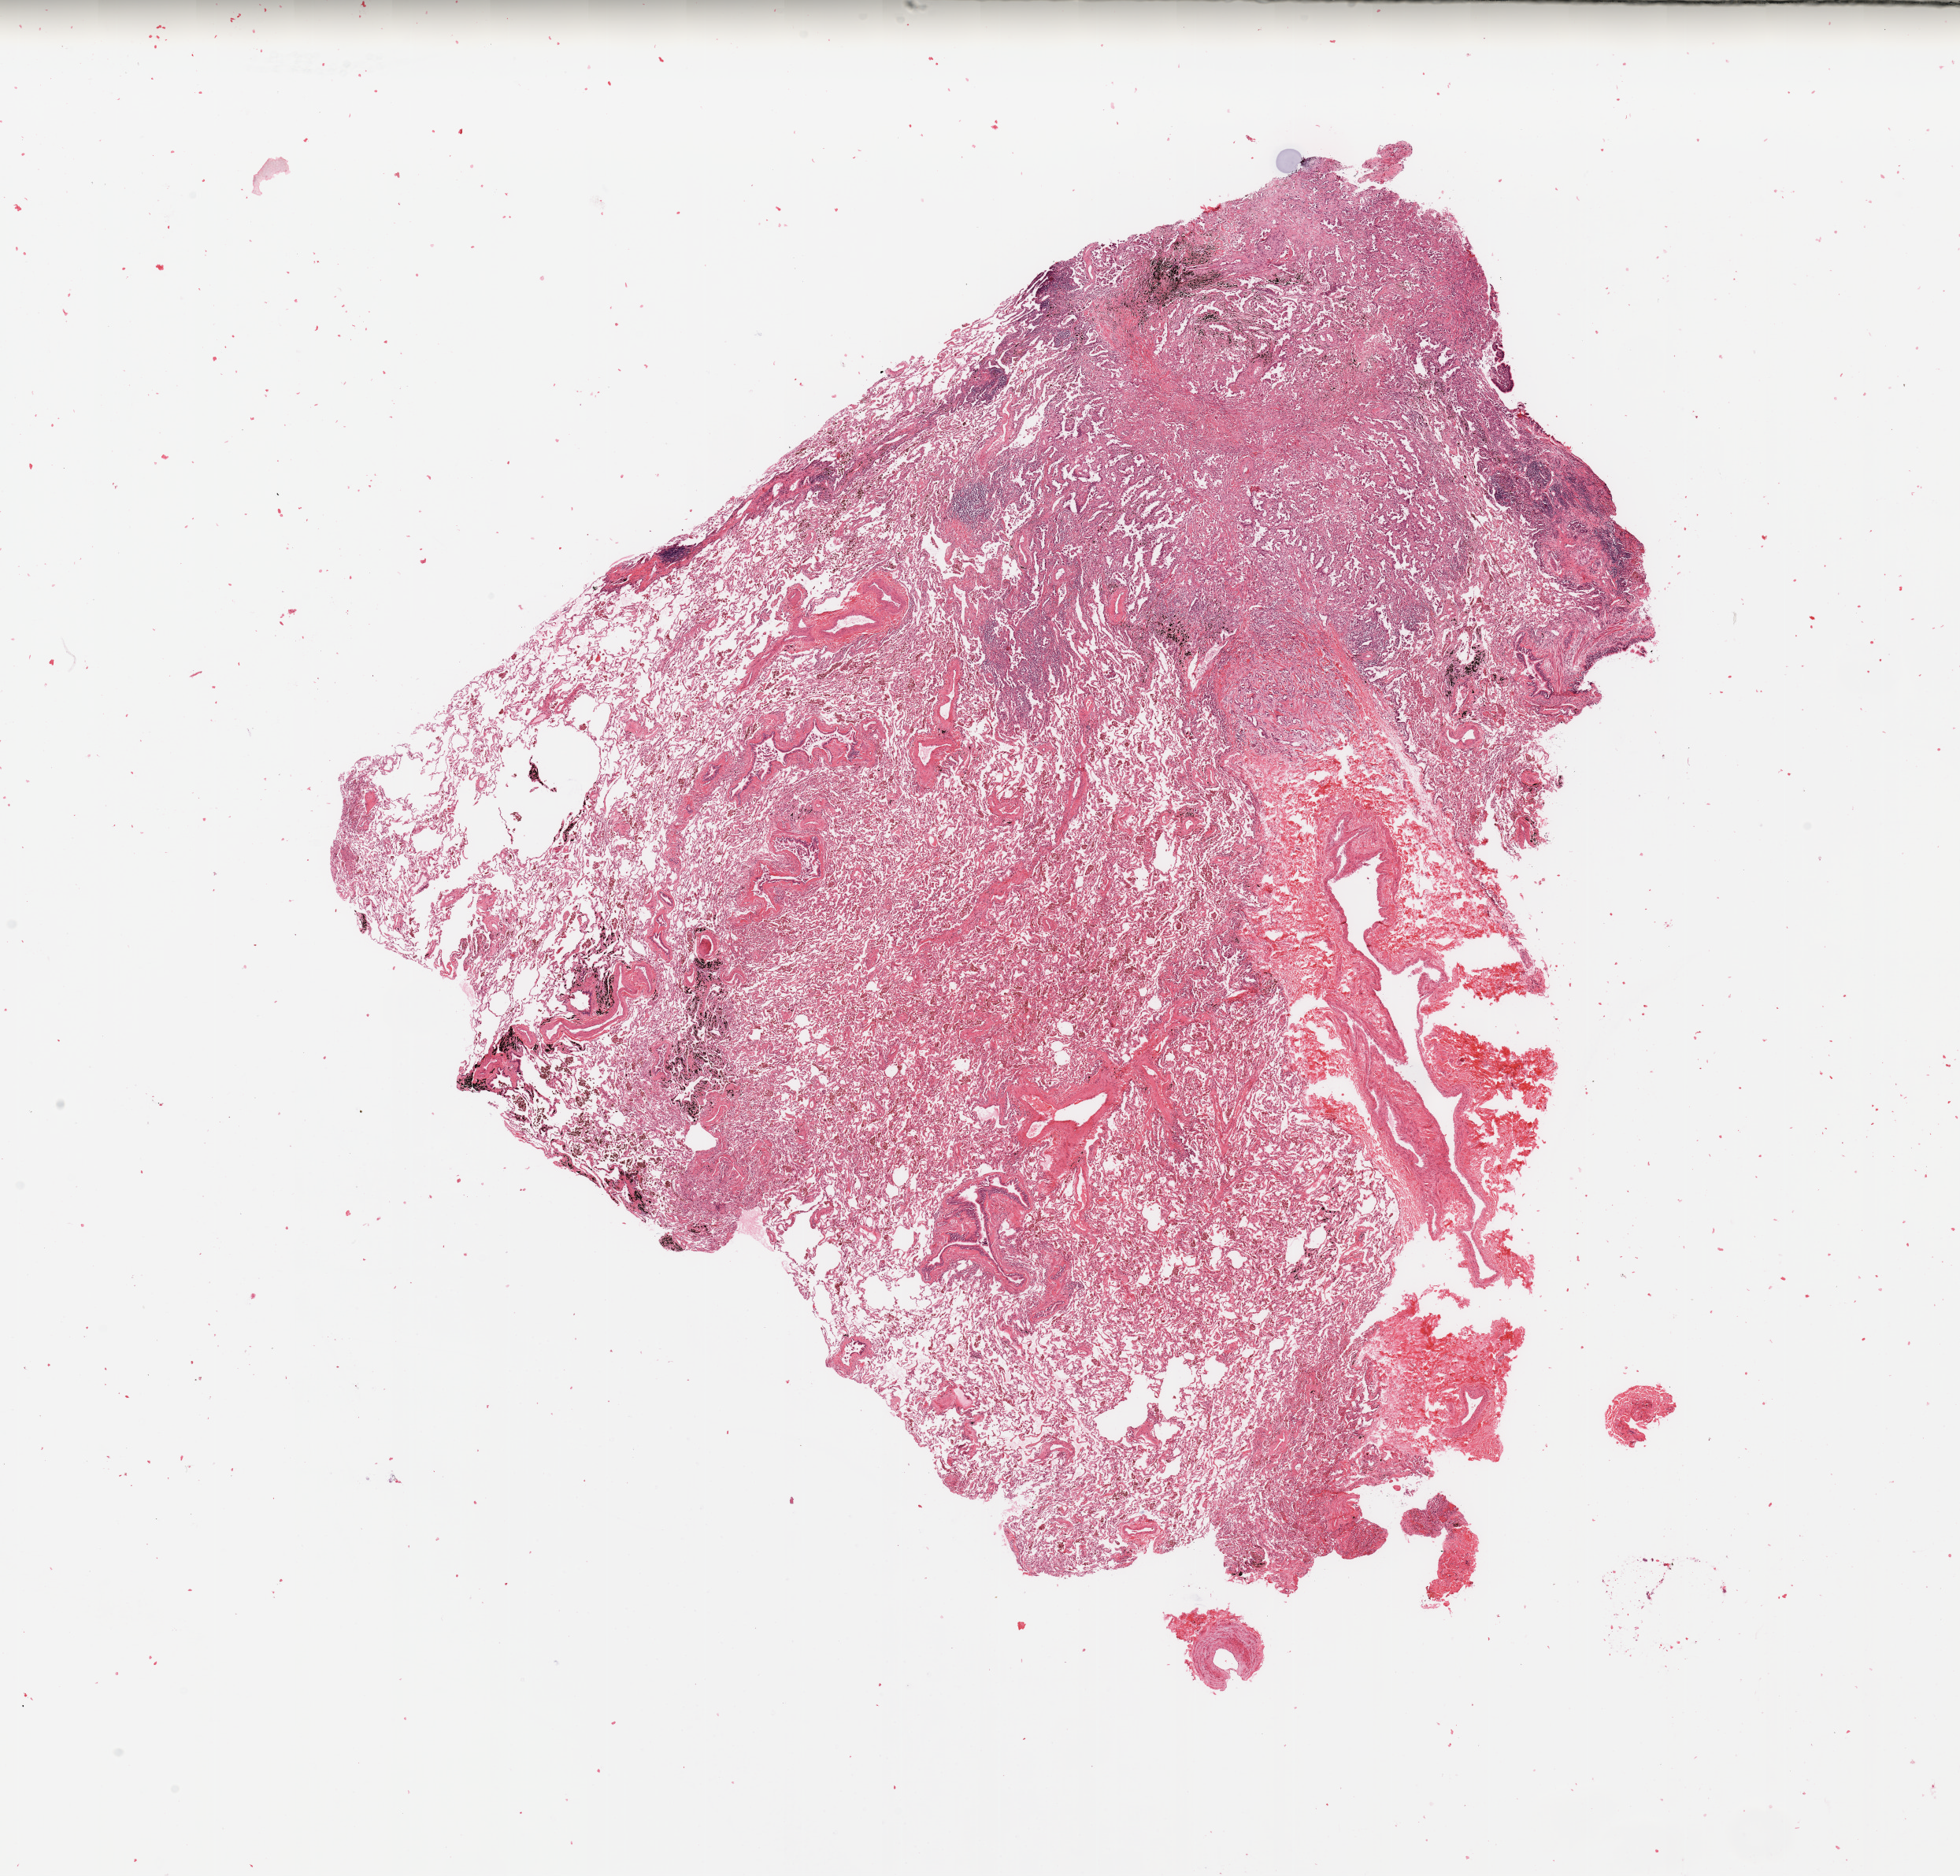
Whole-slide histology image, Hematoxylin and eosin (H&E) stained, a low-resolution overview of the entire scanned area, about 19.7 x 18.8 mm. Tumour tissue sample, sampled site: lung. 59-year-old male patient. Histologic grade: G2 (moderately differentiated). Pathologist review of this section (percent, as recorded): tumour nuclei 30%, necrosis 5%.
• AJCC pathologic stage: IIIA
• diagnosis: Adenocarcinoma, NOS
• primary tumour site (as recorded): right upper lobe